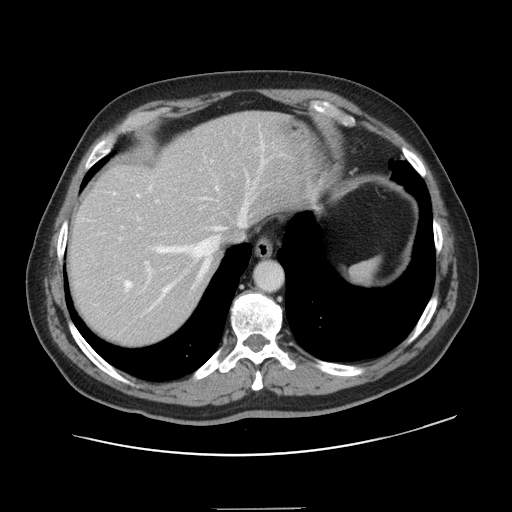
Contrast-enhanced abdominal CT, one axial slice; slice 118 of 143 in the series (ordered by position); 120 kVp; intravenous contrast given; soft-tissue window (W 400 / L 40 HU); 512 × 512 image matrix, field of view 402 × 402 mm. Male patient, age 62 years. From the clinical record (not read from this slice): diagnosis: colorectal cancer liver metastases, imaged before liver resection; multiple liver metastases: yes; largest metastasis: 2.7 cm.
Annotated regions visible in this slice (expert manual segmentation):
- hepatic veins: bounding box <114,186,246,311> (left, top, right, bottom; pixels)
- liver: <70,114,306,345>
- planned liver remnant (the part of the liver to remain after resection): <70,114,305,288>
- portal vein (with intrahepatic branches): <120,133,263,281>